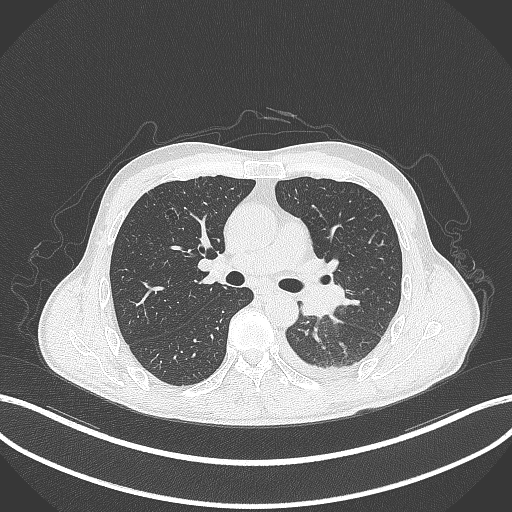
Chest CT, one axial slice; slice 195 of 295 in the series (ordered by position); reconstruction kernel B70f; lung window (W 1500 / L -600 HU); 1 mm slice thickness; 512 × 512 image matrix. Patient: male, 47 years. Case-level facts recorded for this patient, not image findings: clinical TNM (as recorded): T3 N1 M1c; histopathological grade: G3.
Structures marked on this image (bounding box drawn by a radiologist):
- lung tumour (recorded histology: small cell carcinoma): box from (x=299, y=279) to (x=346, y=320) px